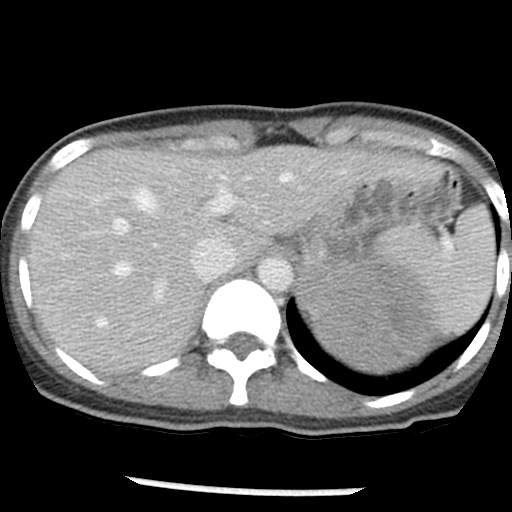
Contrast-enhanced abdominal CT, one axial slice. Slice 38 of 54 in the series (ordered by position). Reconstruction kernel STANDARD. Intravenous contrast given. Soft-tissue window (W 400 / L 40 HU). 5 mm slice thickness. 512 × 512 image matrix, field of view 240 × 240 mm. Female patient, age 33 years. From the clinical record (not read from this slice): diagnosis: adrenocortical carcinoma; tumour side: left adrenal; tumour size at pathology: 11 cm; Ki-67 index: 20 %; stage (as recorded): 2.
Outlined on this slice (semi-automatic segmentation, software-assisted and operator-edited):
- mass: box from (x=300, y=256) to (x=439, y=373) px